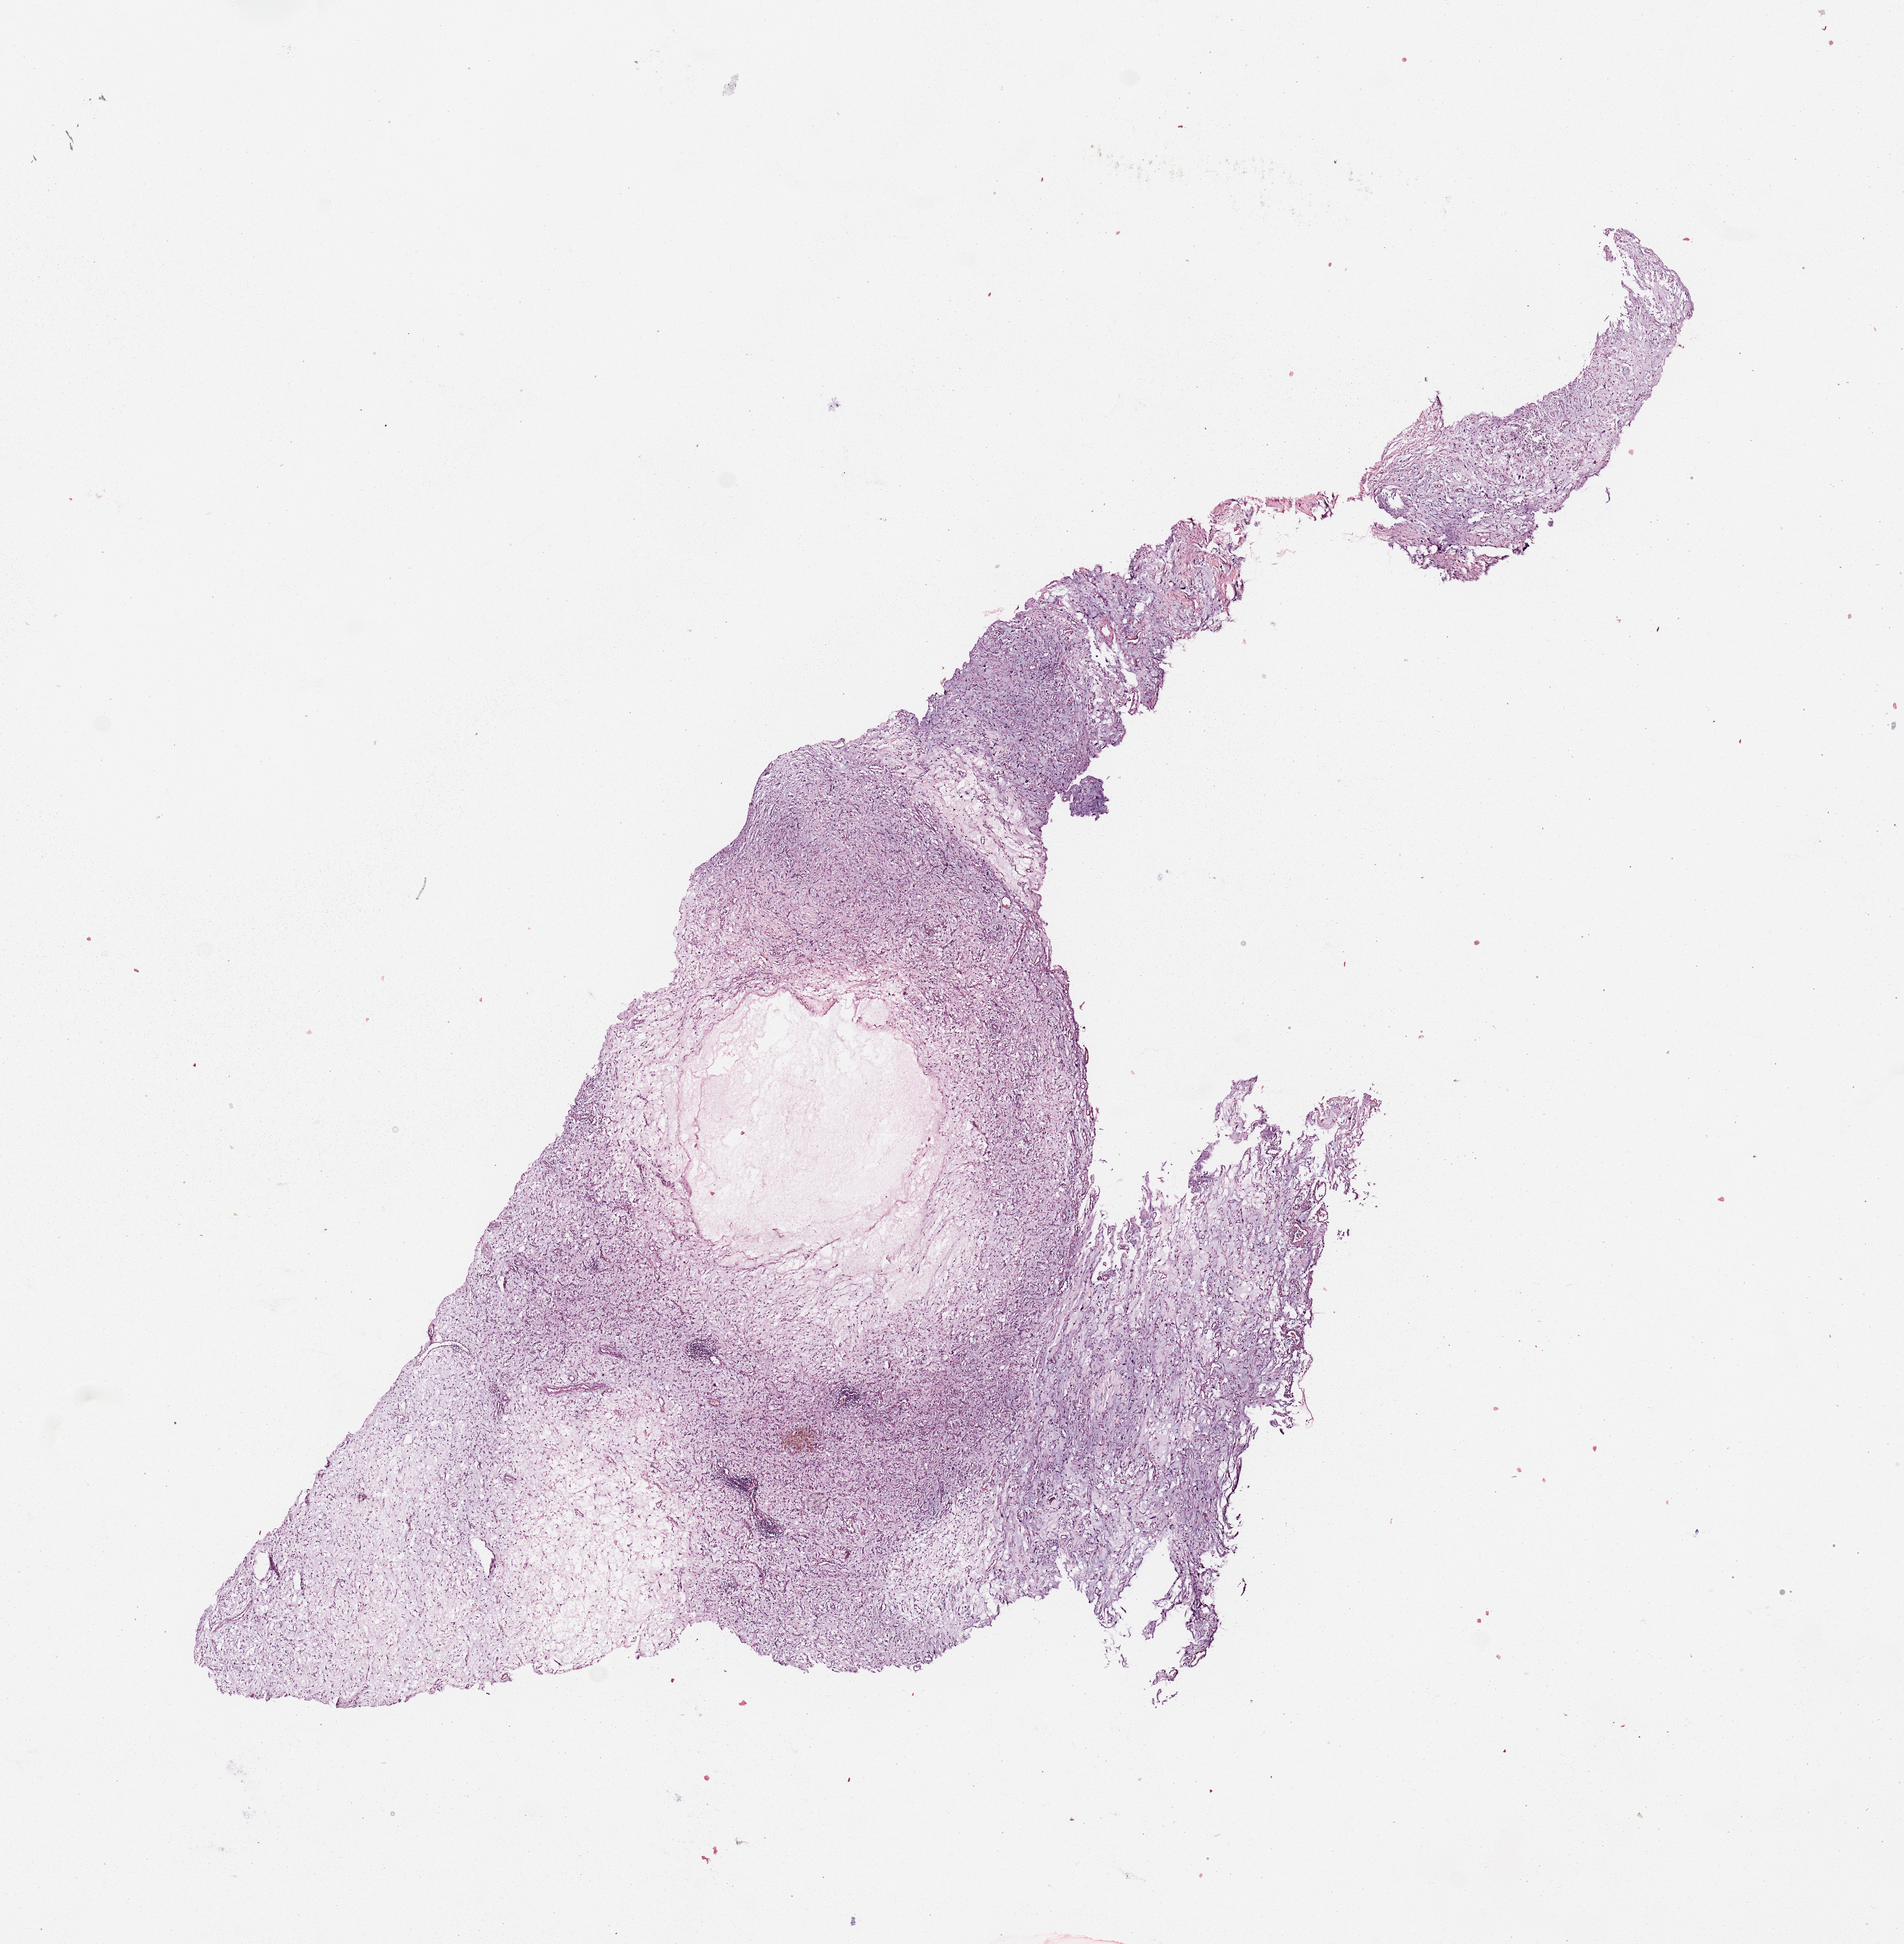
Digitized Hematoxylin and eosin (H&E) stained tissue section (whole slide), low-resolution overview of the scanned area, about 11.8 x 12.1 mm (acquisition: 20x scan). 20-year-old male patient.
Patient diagnosis (cohort enrolment): sarcoma (site not recorded at cohort level).